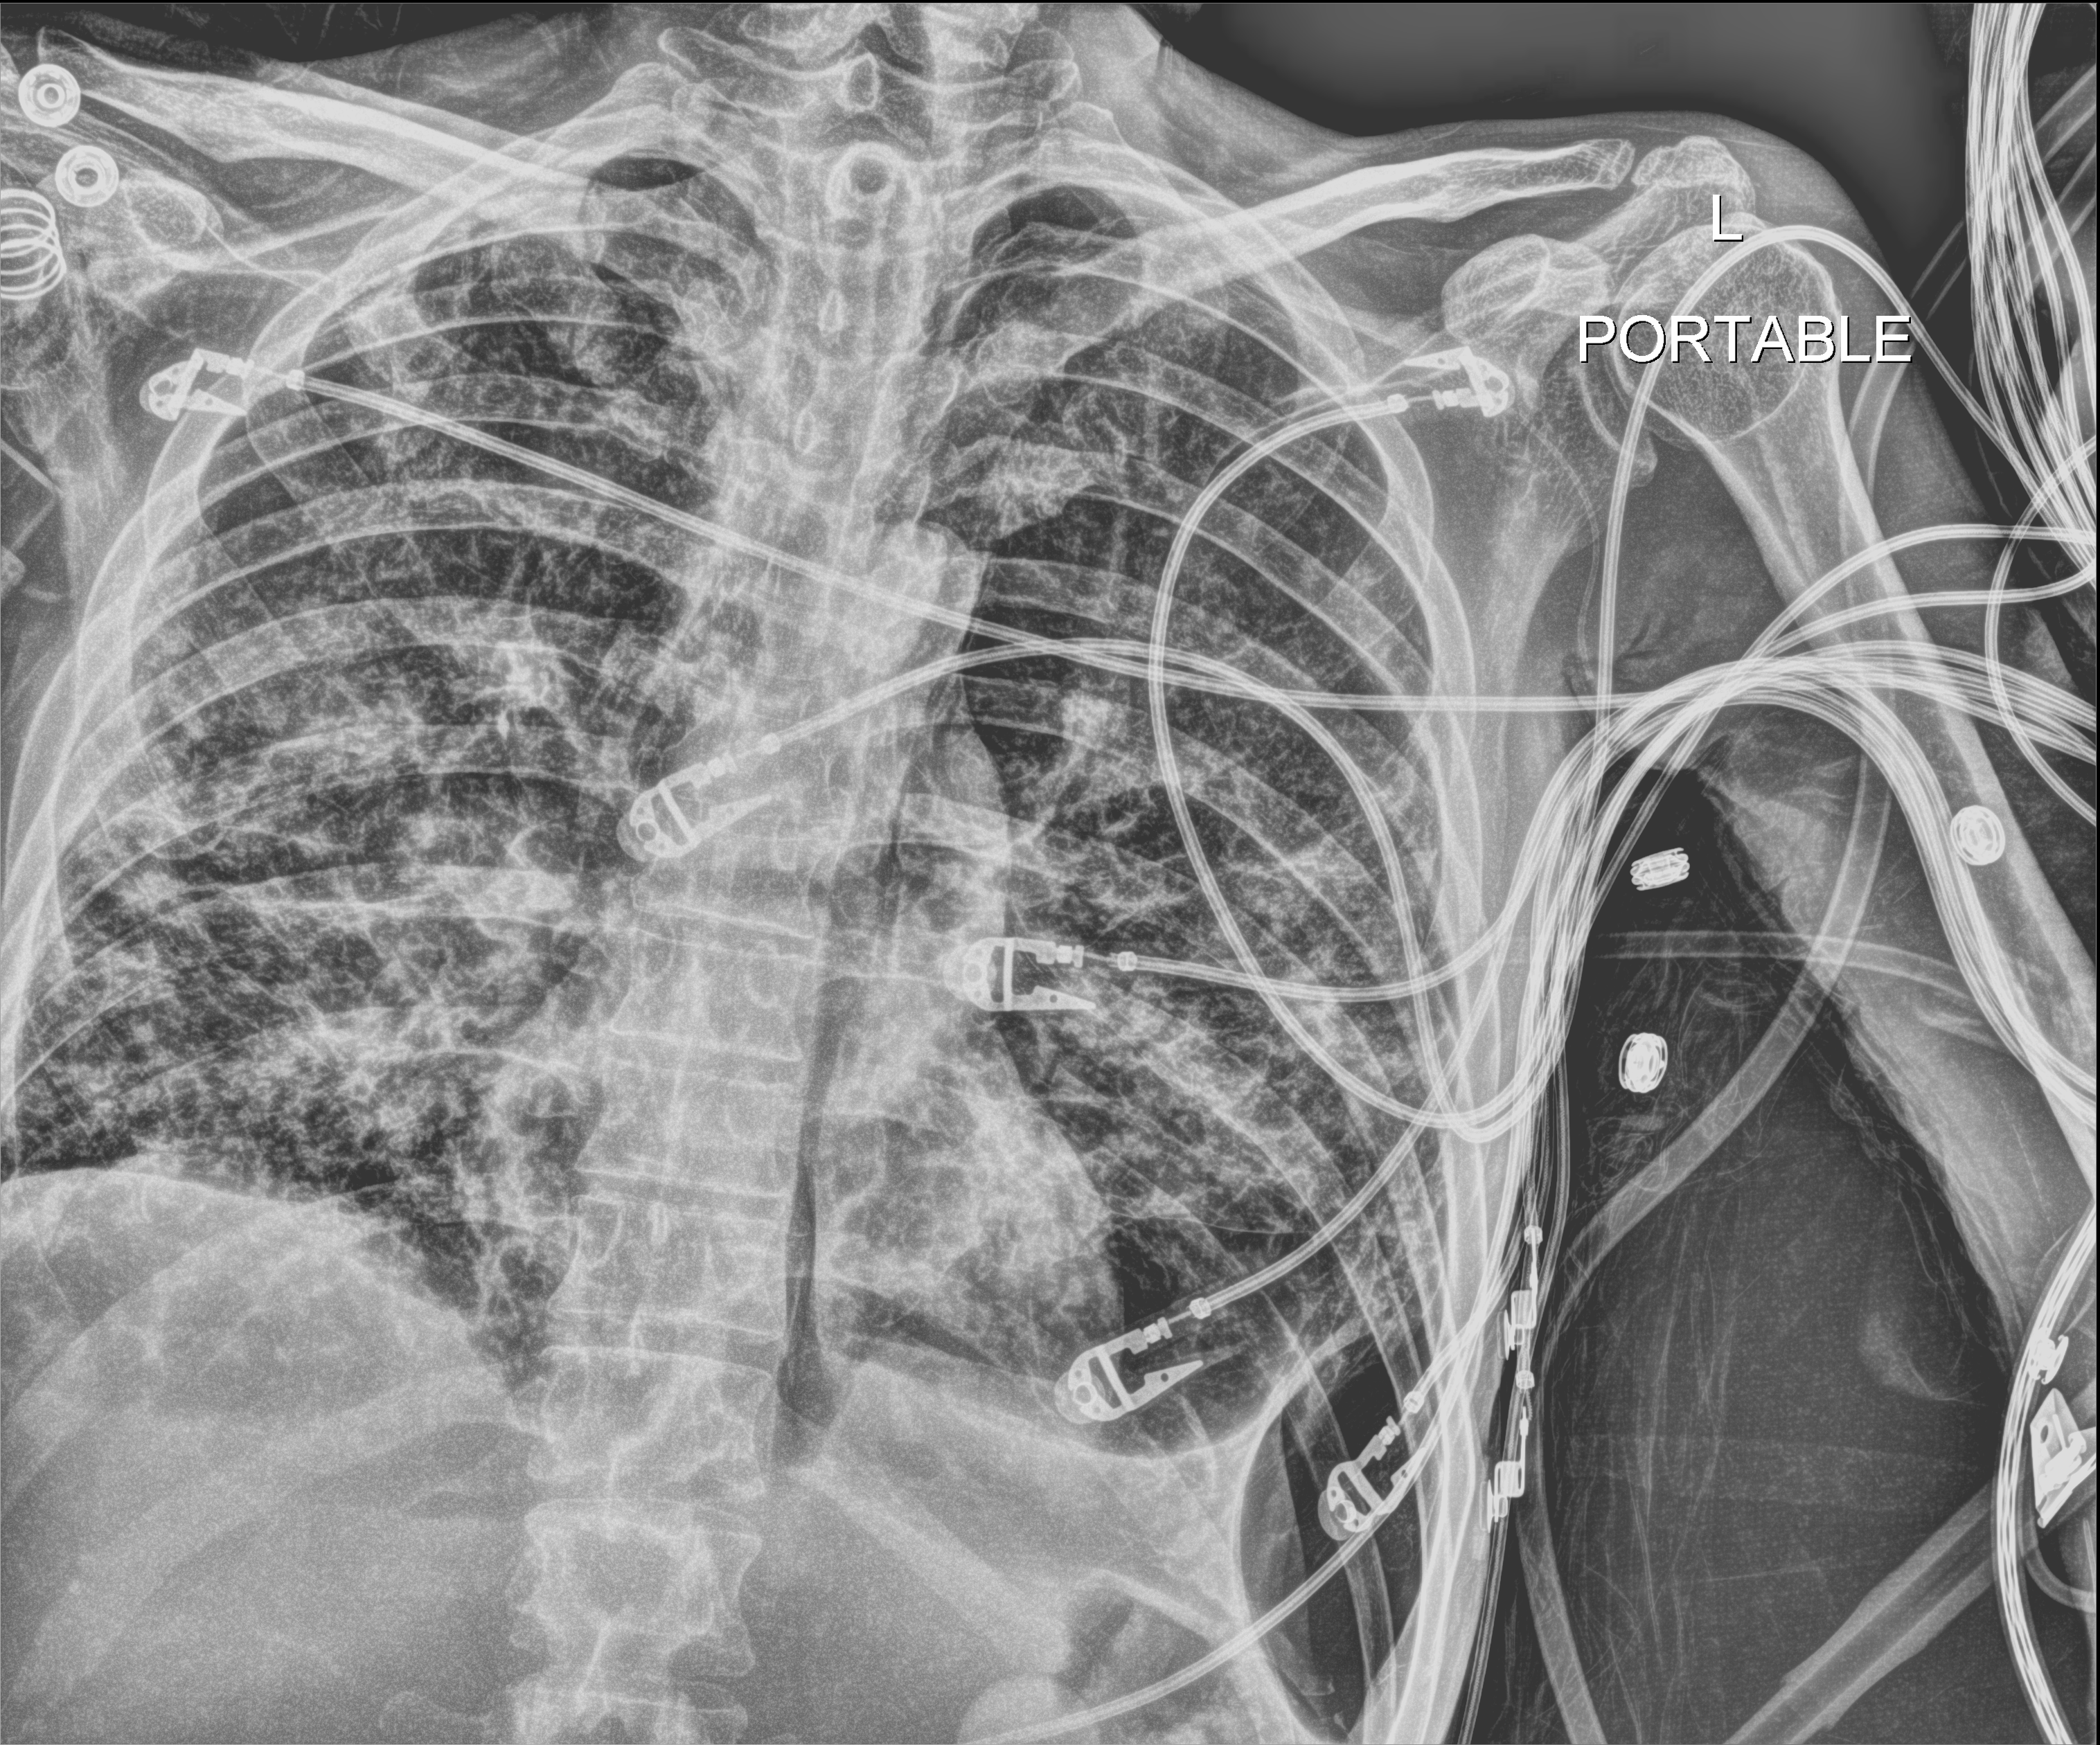
Chest X-ray; anteroposterior (AP) projection. Male patient hospitalised with COVID-19, age 18–59 years.
Admission-level facts for this patient (not findings on this image; timing relative to this image not recorded): mechanically ventilated during this hospital stay: yes; diabetes (admission record): yes.